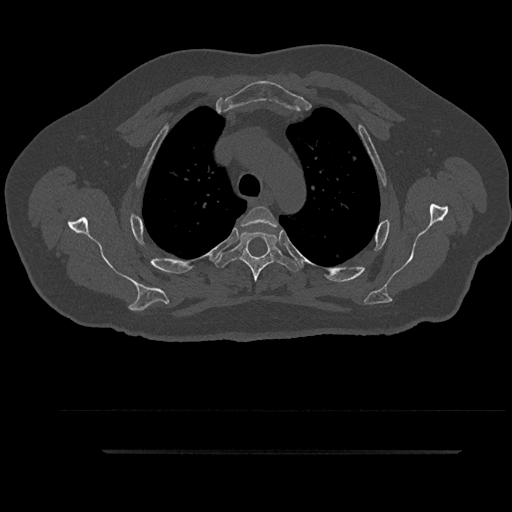
CT including the spine, one axial slice. Position 684 of 797 along the scan axis. 120 kVp. Bone window (W 1800 / L 400 HU). 512 × 512 image matrix, field of view 432 × 432 mm. Patient: male, 63 years. From the clinical record (not read from this slice): primary cancer: renal.
Structures marked on this image (semi-automatically segmented with operator editing):
- T3 vertebra: bounding box [x1, y1, x2, y2] px = [241, 206, 278, 228]
- T4 vertebra: [214, 231, 301, 282]